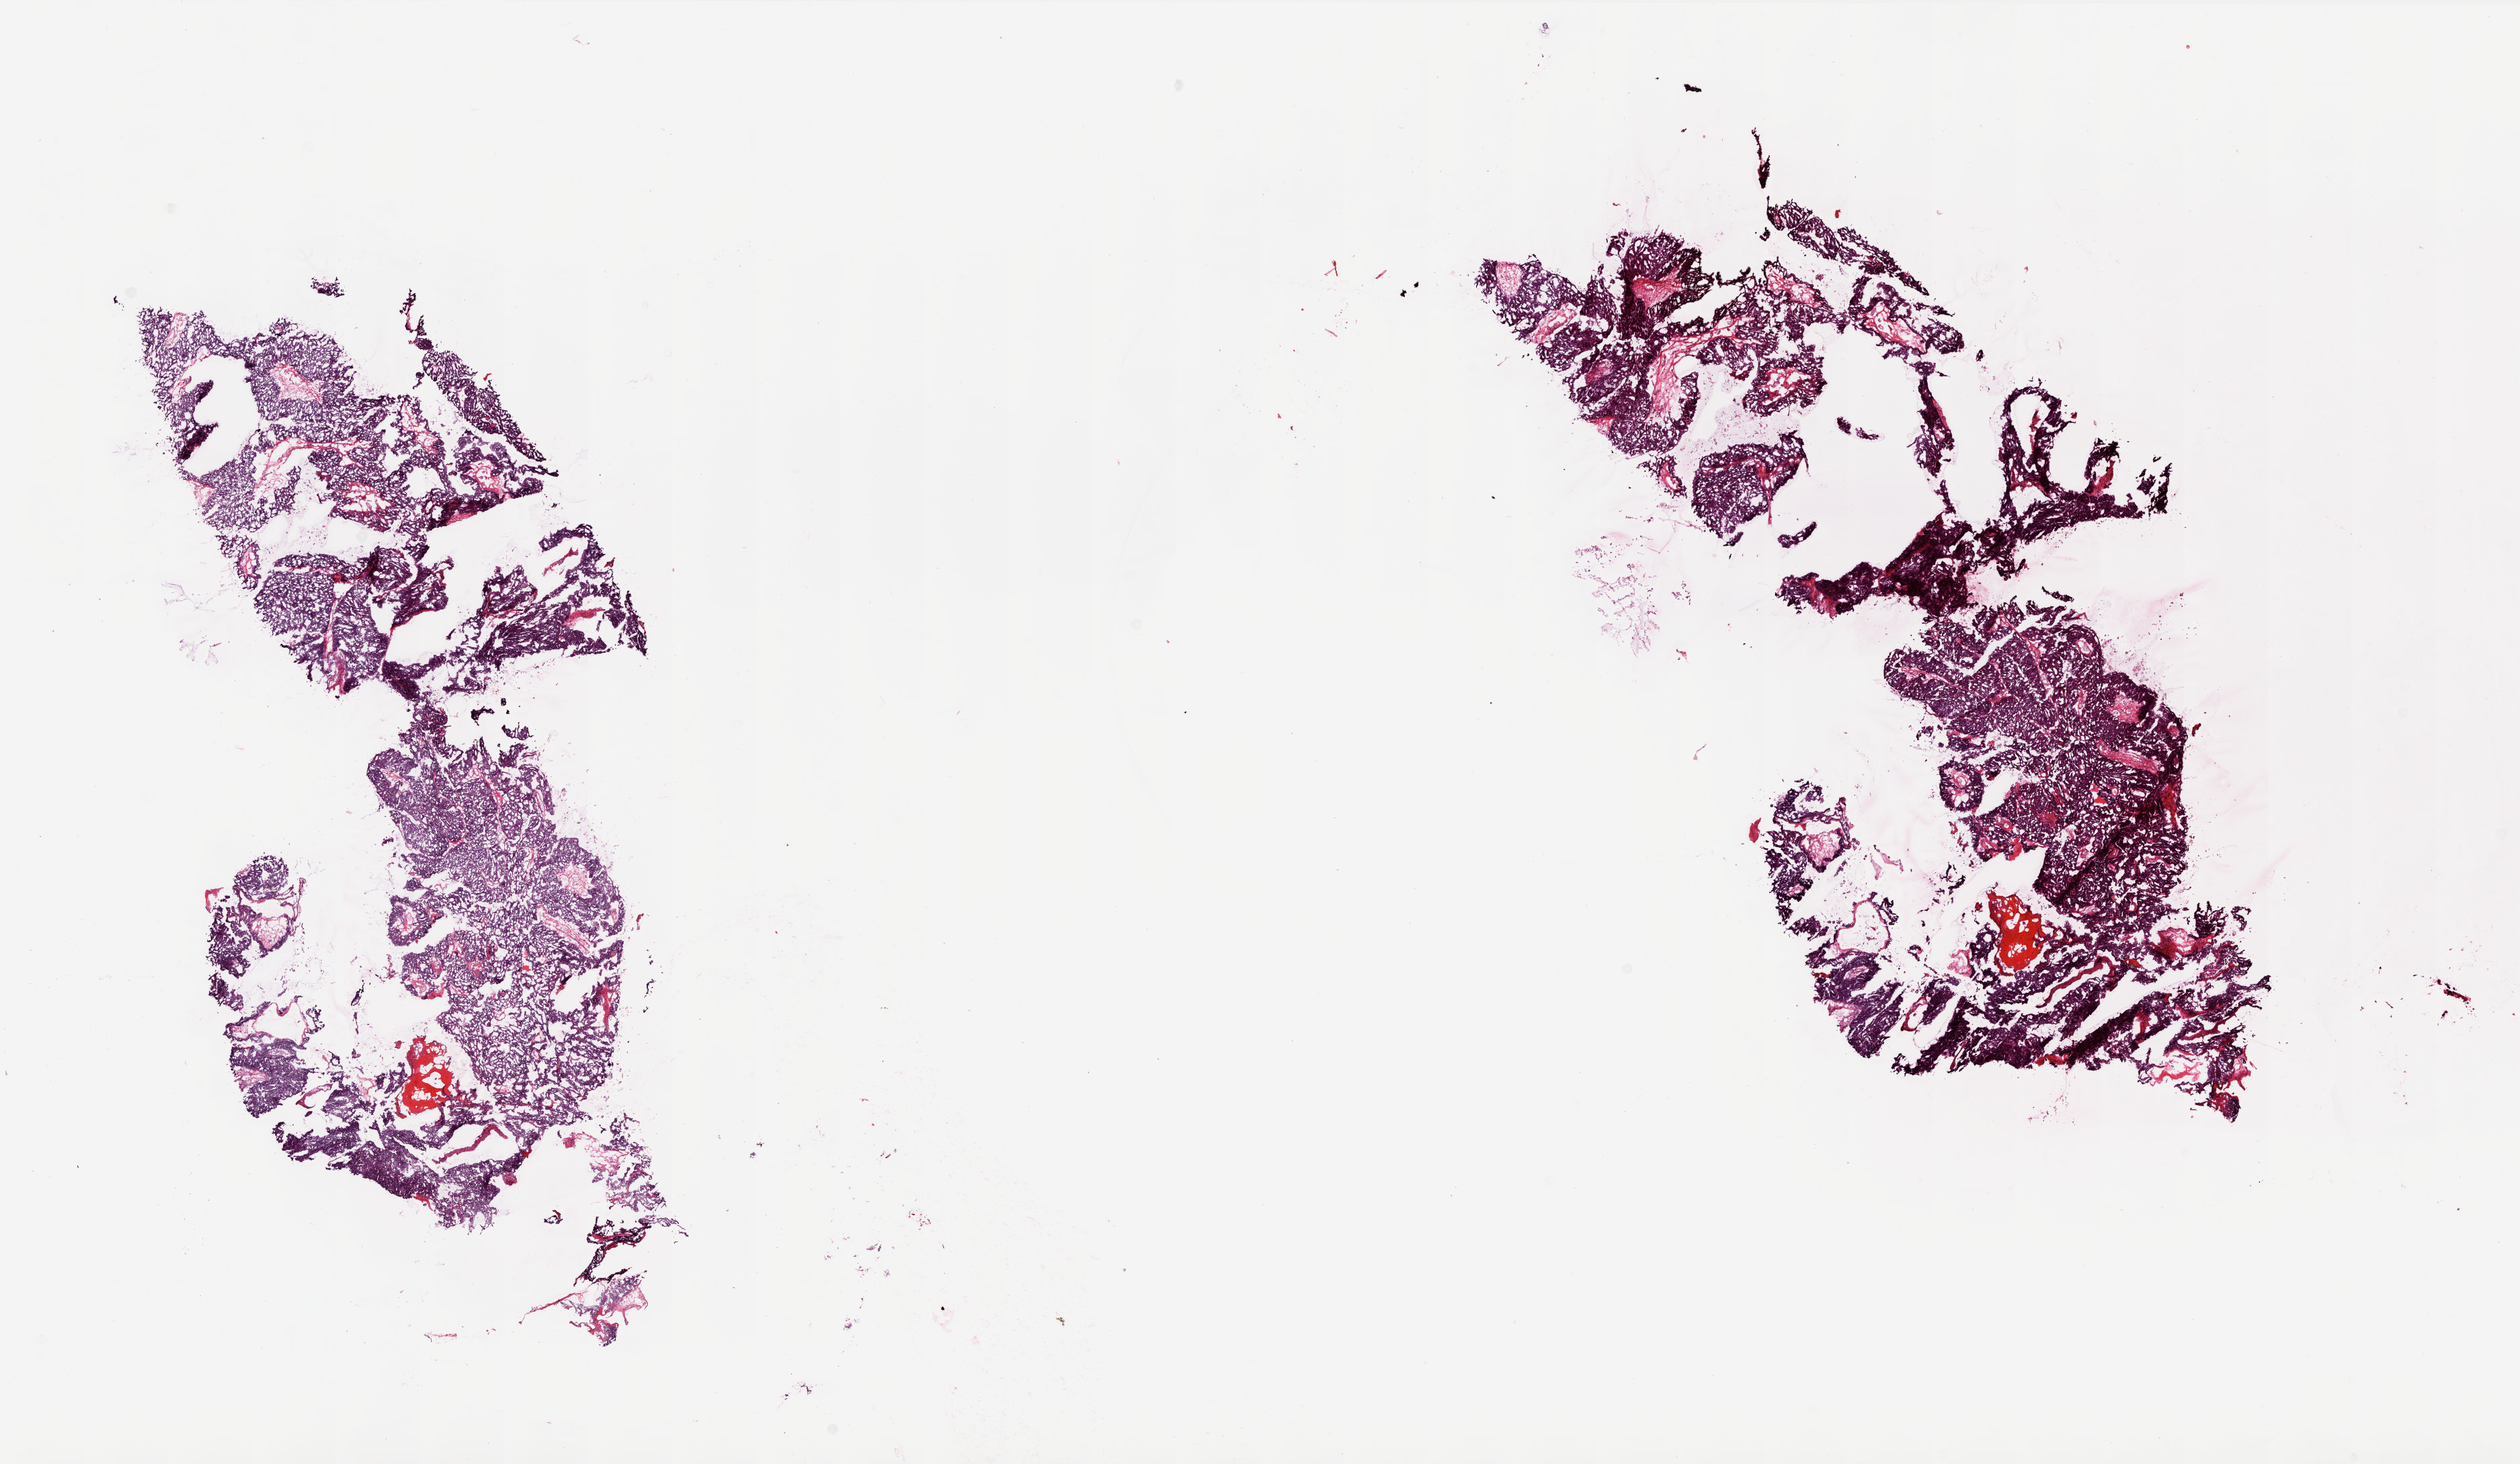
H&E whole-slide image, shown as a low-resolution overview of the whole scanned area (about 29.9 x 17.4 mm), frozen section from the top of the tissue portion, sample: primary tumour, ovary. Patient: female, age at initial diagnosis 46 years. Histologic grade: G3 (poorly differentiated). Pathologist review of this section (percent, as recorded): tumour cells 94%, tumour nuclei 99%, normal cells 0%, stromal cells 5%, necrosis 1%.
- FIGO stage: IIIC
- diagnosis: Serous cystadenocarcinoma, NOS